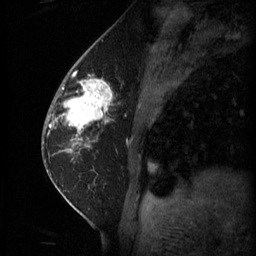
Breast MRI (dynamic contrast-enhanced), one sagittal slice. Slice 23 of 60 in the series (ordered by position). 3 images stored at this slice position (order not interpretable as contrast timing). 1.5 T. TE 4.2 ms, TR 11 ms. 256 × 256 image matrix, field of view 180 × 180 mm. Patient: female, 62 years.
Structures marked on this image (semi-automatic segmentation, software-assisted and operator-edited):
- analysis volume of interest (the breast-tissue region the enhancement analysis was run in; not a lesion): bounding box <55,72,113,135> (left, top, right, bottom; pixels)
- tumour enhancement mask (voxels above the 70 % enhancement threshold inside the analysis volume of interest): <57,80,113,135>